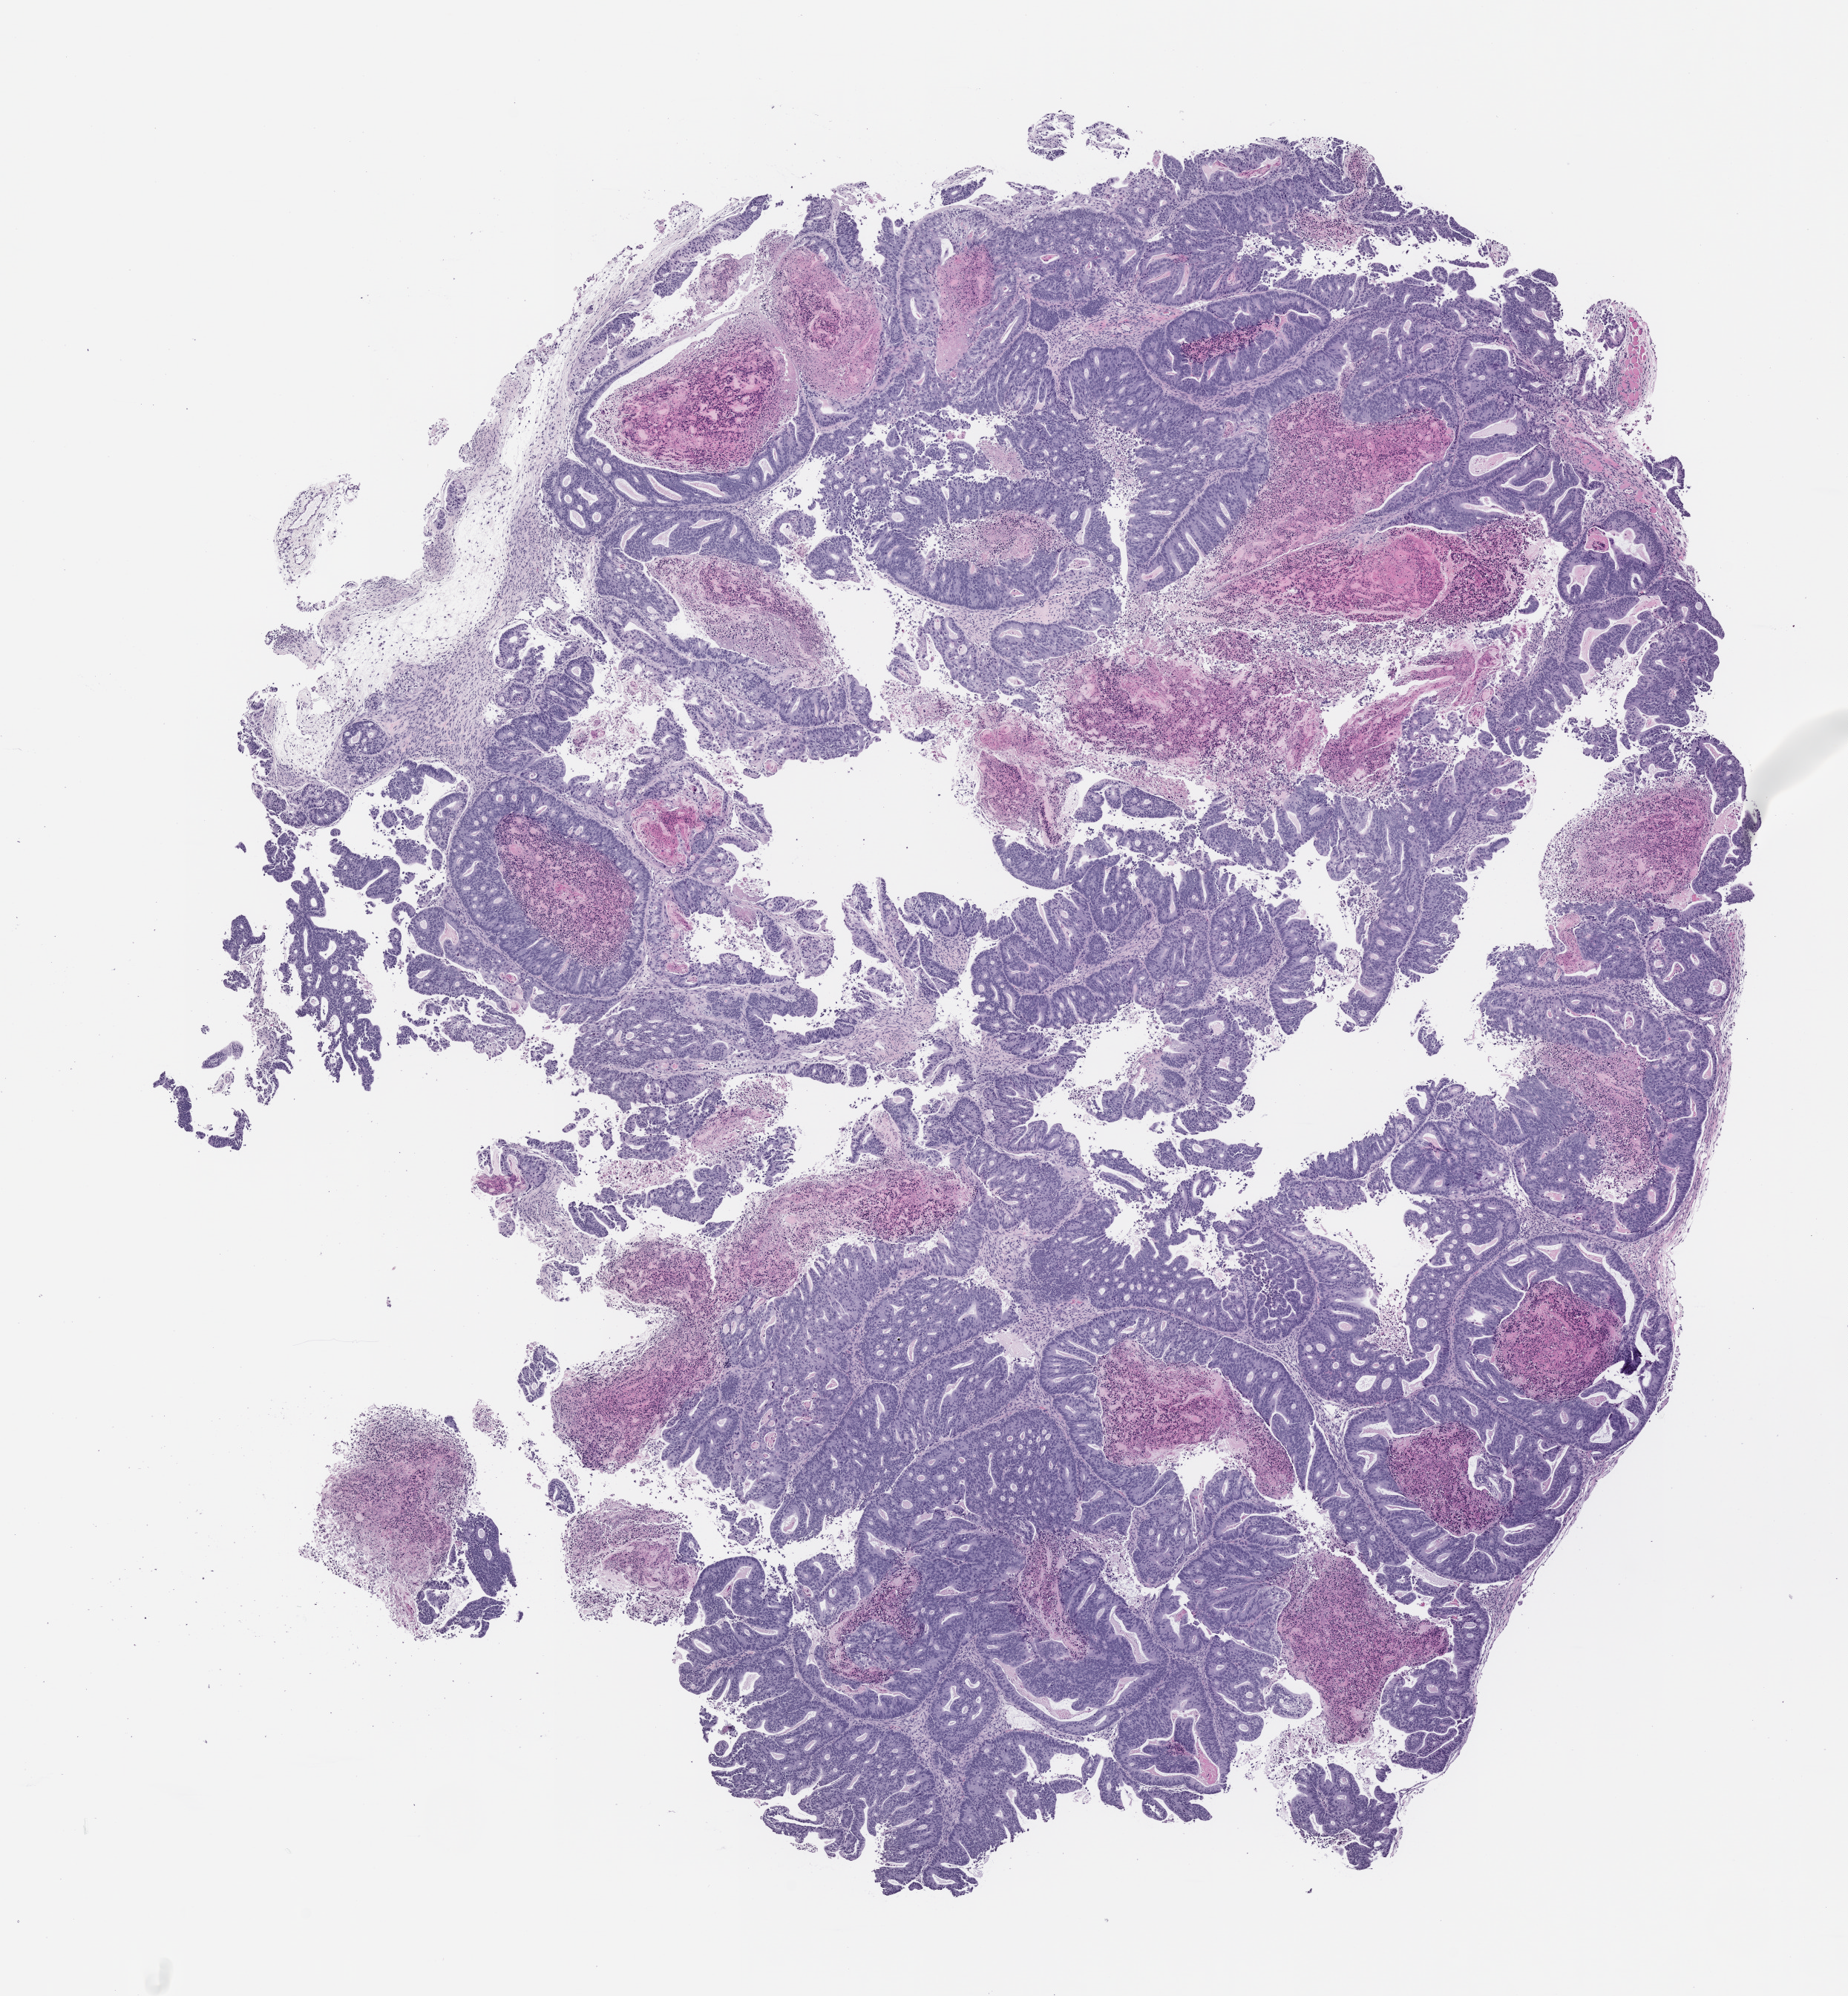
Whole-slide image, H&E: patient-derived xenograft (human tumor grown in a mouse), passage 2 — low-resolution overview of the scanned area, about 10.0 x 10.8 mm, formalin-fixed, paraffin-embedded (FFPE) tissue, tumor site category: colon.
Originating patient diagnosis: Colon Adenocarcinoma.